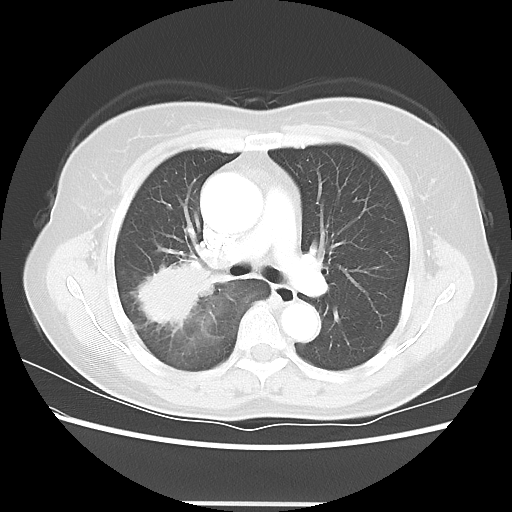
Chest CT, one axial slice. Slice 37 of 56 in the series (ordered by position). Lung window (W 1500 / L -600 HU). 5 mm slice thickness. 512 × 512 image matrix, field of view 360 × 360 mm. Female patient, age 55 years. From the clinical record (not read from this slice): clinical TNM (as recorded): T2 N1 M0; histopathological grade: G2-3.
Outlined on this slice (bounding box drawn by a radiologist):
- lung tumour (recorded histology: adenocarcinoma): box from (x=124, y=256) to (x=222, y=339) px